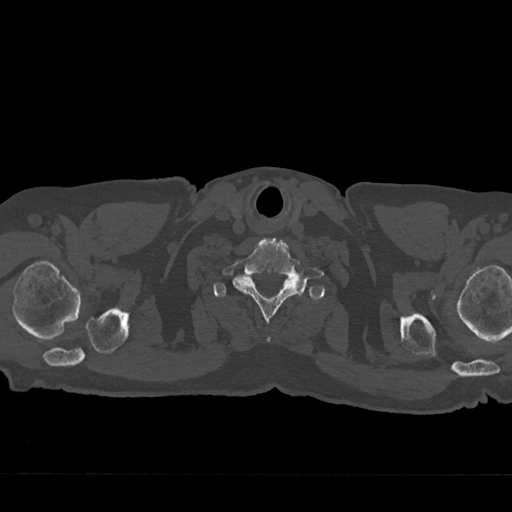
CT including the spine, one axial slice. Slice 686 of 797 in the series (ordered by position). Reconstruction kernel Br40s/3. Bone window (W 1800 / L 400 HU). 0.5 mm slice thickness. 512 × 512 image matrix, field of view 377 × 377 mm. Male patient, age 75 years. Case-level facts recorded for this patient, not image findings: primary cancer: renal; vertebrae with lytic lesions (as recorded): T4.
Structures marked on this image (semi-automatic segmentation, software-assisted and operator-edited):
- T1 vertebra: bounding box (x1, y1, x2, y2) in pixels: (214, 277, 303, 298)